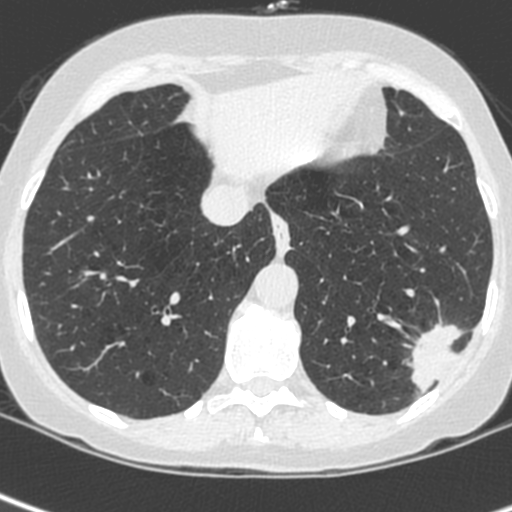
Low-dose screening chest CT, axial slice, first (baseline) screen, lung window (W 1500 / L -600 HU), standard (soft-tissue) reconstruction kernel (C), 120 kVp, slice 173 of 252 in the series. Female participant, aged 56 years at enrolment. Current smoker at enrolment.
• Expert reader's lesion annotation, box from (x=405, y=315) to (x=477, y=387) px.
• The exam's reader record, not a measurement of the box and not confirmed to be the same lesion: non-calcified nodule or mass ≥4 mm, left lower lobe, 37 × 29 mm, spiculated (stellate) margins, ground glass attenuation.
• Official screen result: positive, change unspecified: nodule(s) >= 4 mm or enlarging nodule(s), mass(es), or other non-specific abnormalities suspicious for lung cancer.